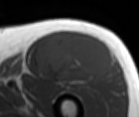
MRI of an extremity soft-tissue mass, one axial slice. Position 60 of 86 along the scan axis. MR volume resampled by the dataset authors to the PET/CT grid (not the native acquisition matrix). 3.27 mm slice thickness. 139 × 117 image matrix. Male patient. From the clinical record (not read from this slice): histological type: extraskeletal osteosarcoma; grade: high; site of the primary tumour: thigh.
Outlined on this slice (expert contour drawn on MRI and transferred to this co-registered scan by the dataset authors):
- gross tumour volume (mass): bounding box <36,32,114,83> (left, top, right, bottom; pixels)